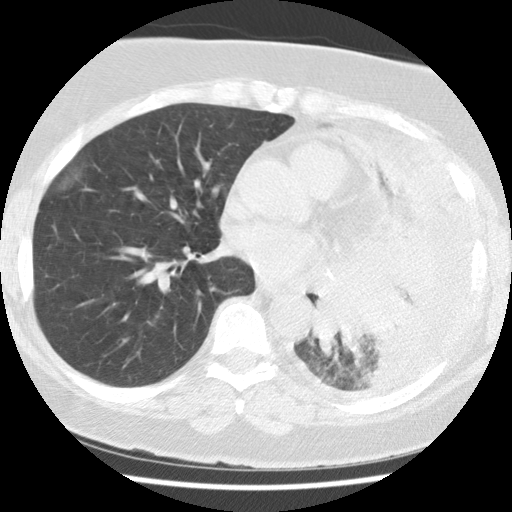
Axial slice from a low-dose chest CT screening exam; first (baseline) screen; lung window (W 1500 / L -600 HU); standard (soft-tissue) reconstruction kernel (STANDARD); 120 kVp; 512 × 512 image matrix. Female participant, aged 65 years at enrolment.
- Expert reader's lesion annotation, bounding box [x1, y1, x2, y2] px = [305, 282, 415, 372].
- Reader record for this screening exam (exam-level; its link to the box is not recorded): non-calcified nodule or mass ≥4 mm, left lower lobe, 74 × 48 mm, spiculated (stellate) margins, soft tissue attenuation.
- Official screen result: positive, change unspecified: nodule(s) >= 4 mm or enlarging nodule(s), mass(es), or other non-specific abnormalities suspicious for lung cancer.
- Lung cancer was diagnosed 13 days after this screen: adenocarcinoma, NOS, left lower lobe, stage IV (AJCC 6th edition), 74 mm at pathology.